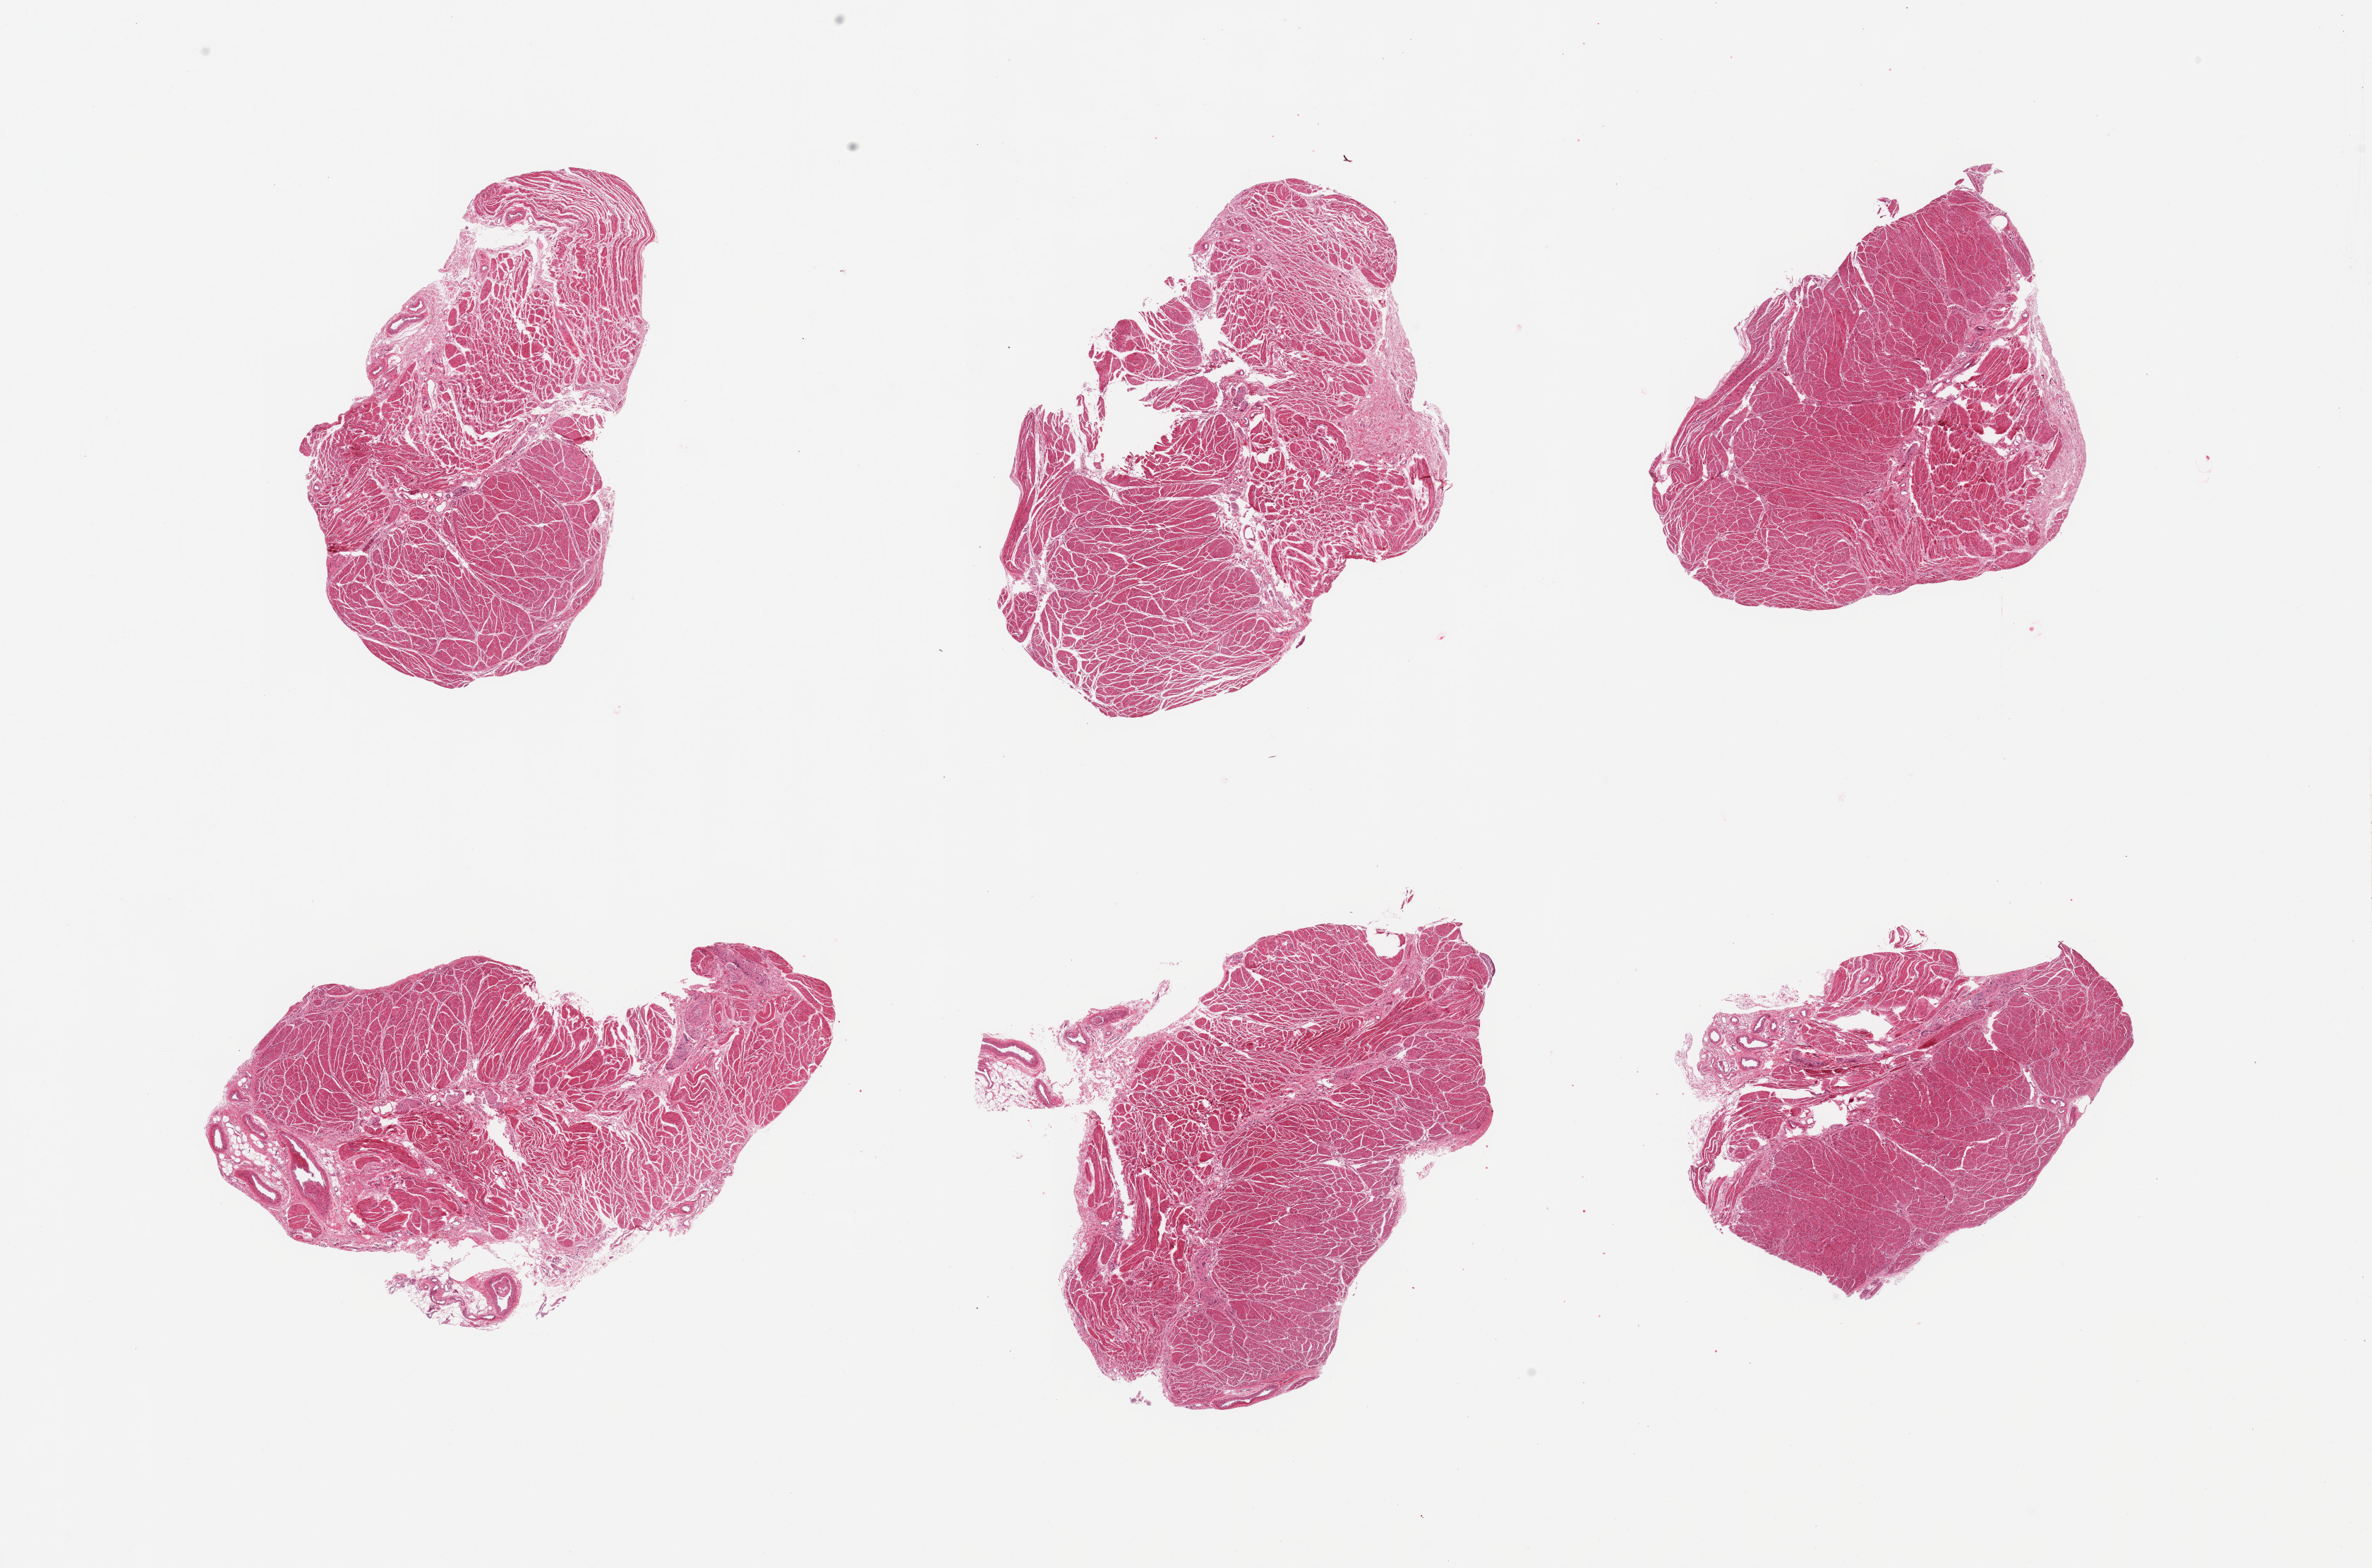
Whole-slide image, haematoxylin and eosin stain — whole scanned area (about 26.6 x 17.6 mm, from a 20x scan) shown as a low-resolution overview. PAXgene-fixed paraffin-embedded (PFPE) section. Section of gastroesophageal junction (target tissue). Tissue donor sample. Female donor.
Review note (as recorded): 6 pieces; target muscularis with small portion of submucosa.